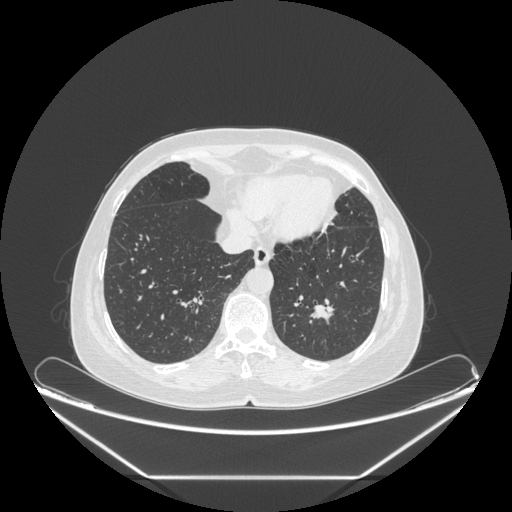
Chest CT, one axial slice; slice 71 of 241 in the series (ordered by position); lung window (W 1500 / L -600 HU); 1.25 mm slice thickness; 512 × 512 image matrix. Female patient, age 63 years. From the clinical record (not read from this slice): clinical TNM (as recorded): T1c N0 M0.
Outlined on this slice (bounding box drawn by a radiologist):
- lung tumour (recorded histology: adenocarcinoma): bounding box <313,298,341,330> (left, top, right, bottom; pixels)